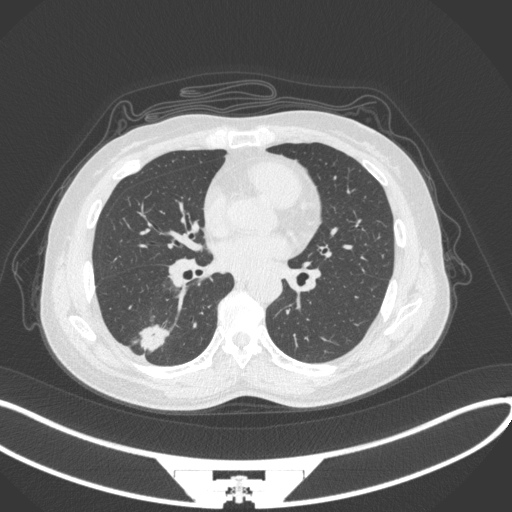
Chest CT, one axial slice. Slice 139 of 352 in the series (ordered by position). Reconstruction kernel B31f. 120 kVp. Lung window (W 1500 / L -600 HU). 1 mm slice thickness. 512 × 512 image matrix, field of view 400 × 400 mm. Female patient, age 55 years. Case-level facts recorded for this patient, not image findings: clinical TNM (as recorded): T1c N1 M0.
Annotated regions visible in this slice (rectangle marked by the reading radiologist):
- lung tumour (recorded histology: adenocarcinoma): box from (x=133, y=320) to (x=174, y=353) px